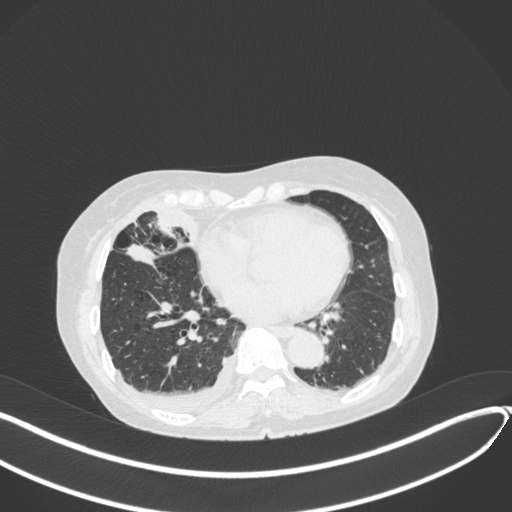
Chest CT, one axial slice; position 150 of 418 along the scan axis; reconstruction kernel B31f; 120 kVp; lung window (W 1500 / L -600 HU); 512 × 512 image matrix, field of view 400 × 400 mm. Female patient, age 75 years. From the clinical record (not read from this slice): clinical TNM (as recorded): T2a N3 M0.
Annotated regions visible in this slice (rectangle marked by the reading radiologist):
- lung tumour (recorded histology: adenocarcinoma): bounding box (x1, y1, x2, y2) in pixels: (125, 239, 158, 268)